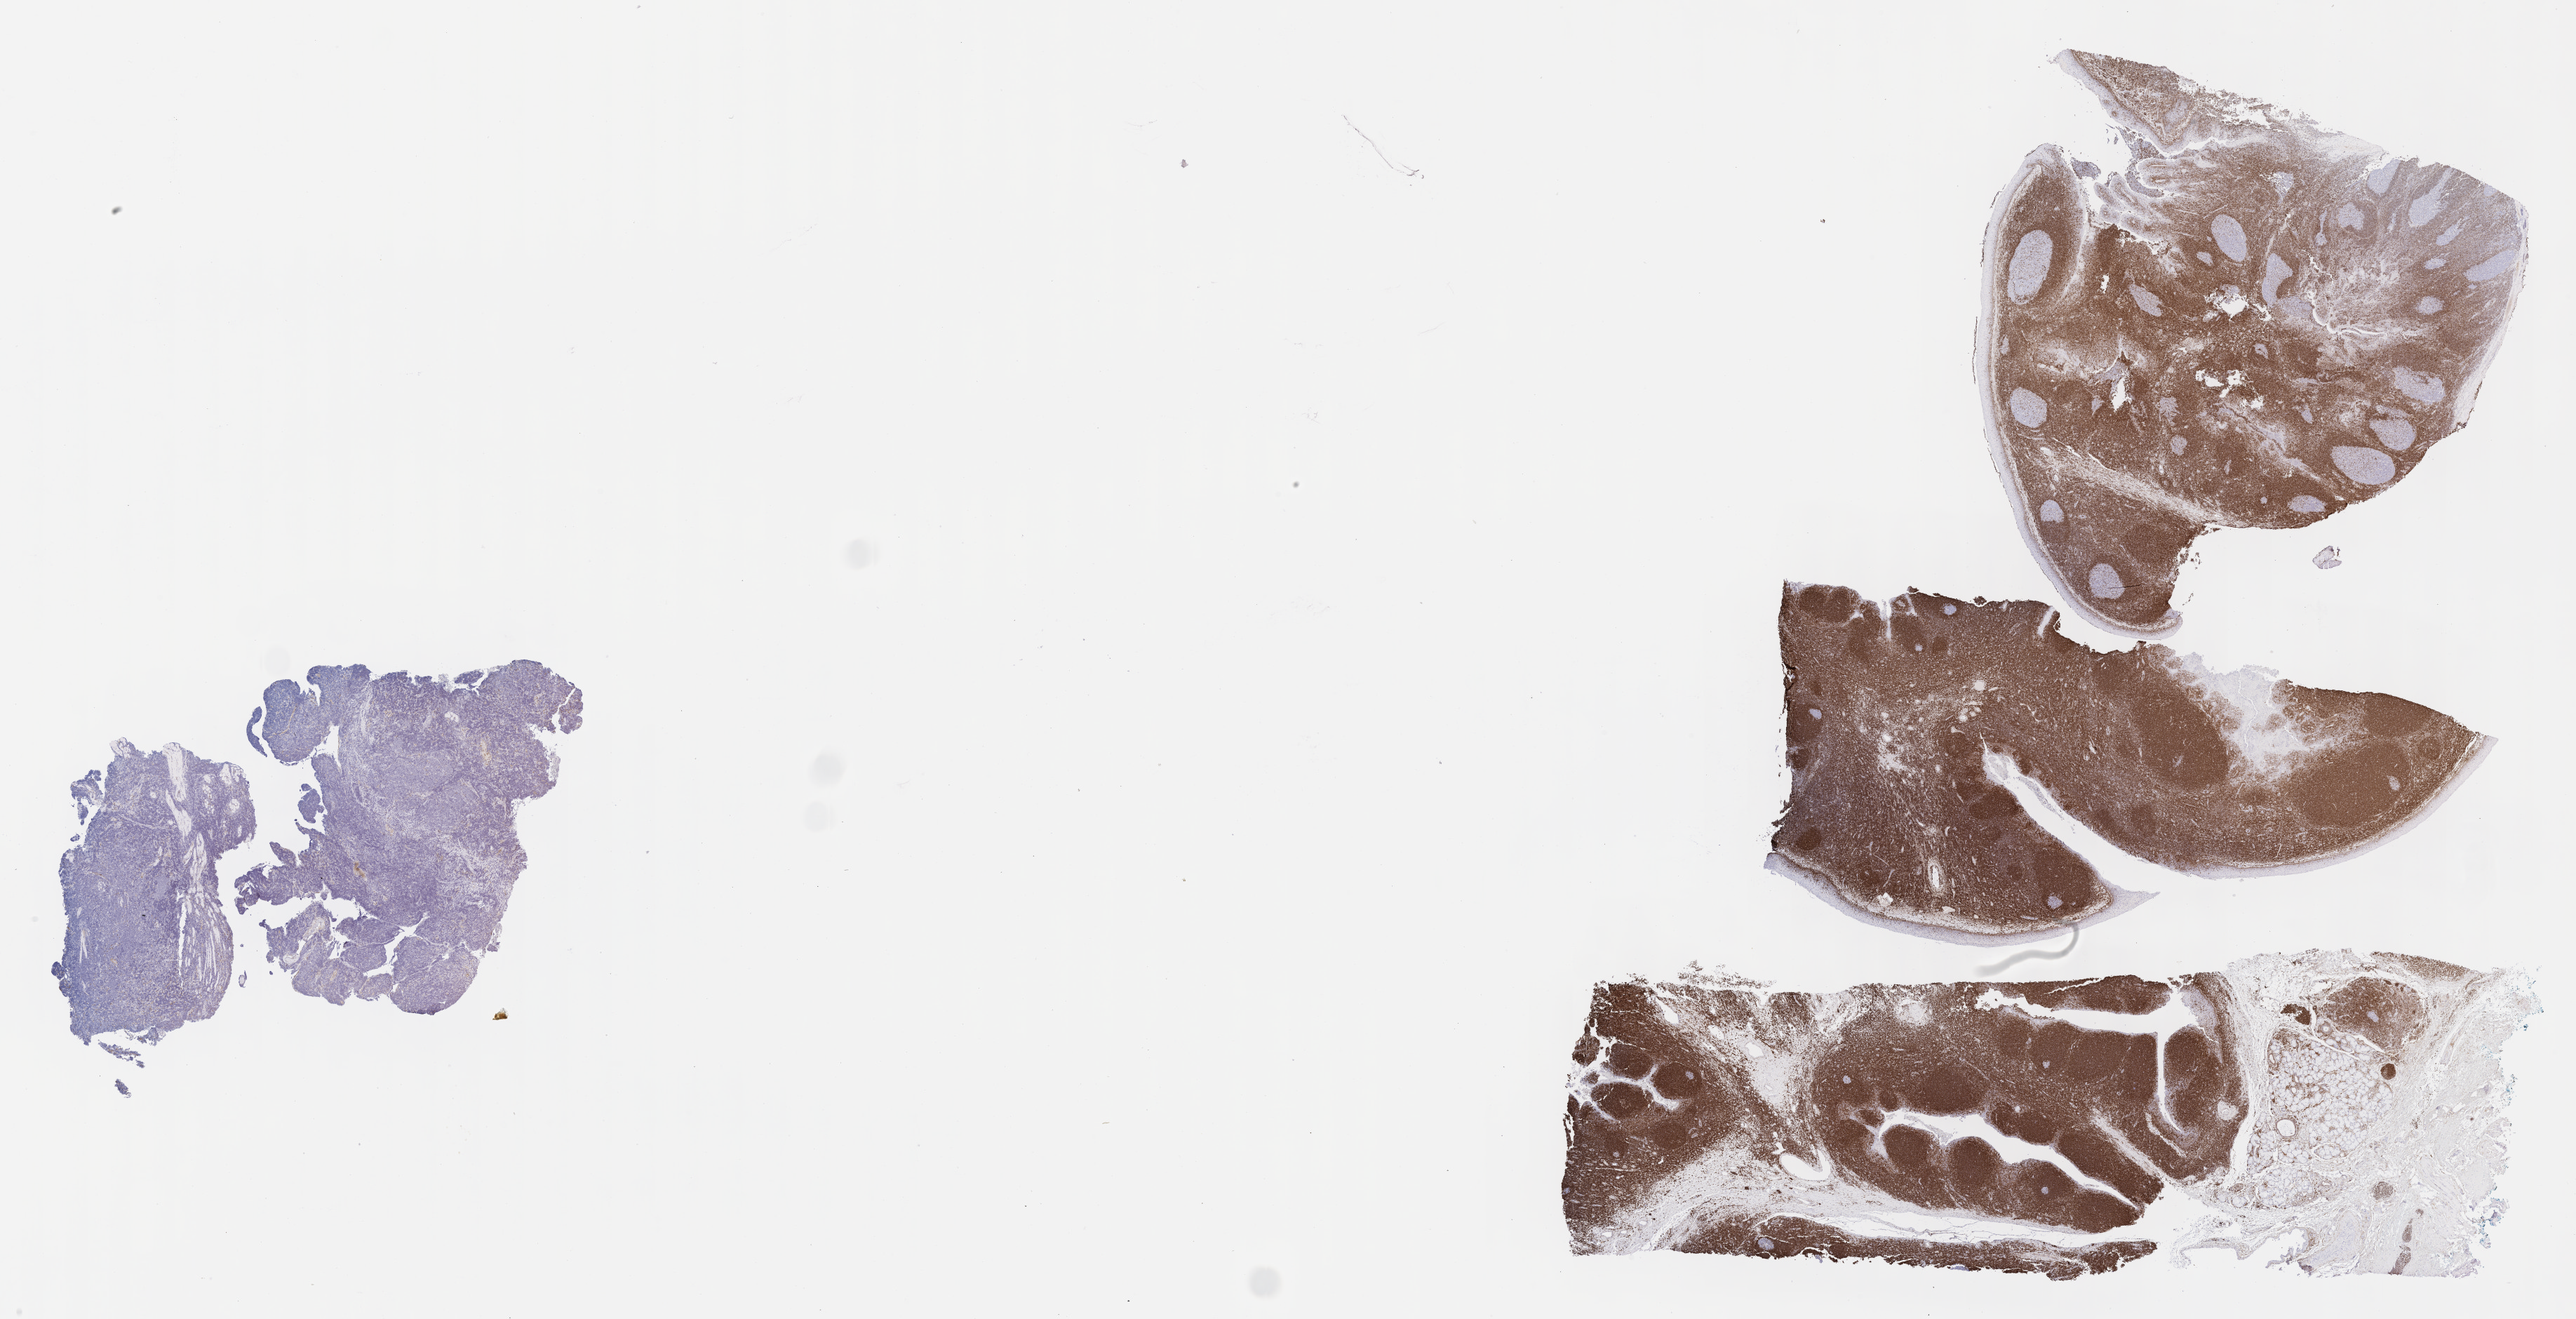
IHC for BCL2, whole-slide image, whole scanned area (about 29.7 x 15.2 mm) shown as a low-resolution overview, specimen: tumor tissue, anatomic site: cranium. Male patient; age at initial diagnosis 8 years.
Diagnosis: Burkitt lymphoma, NOS.